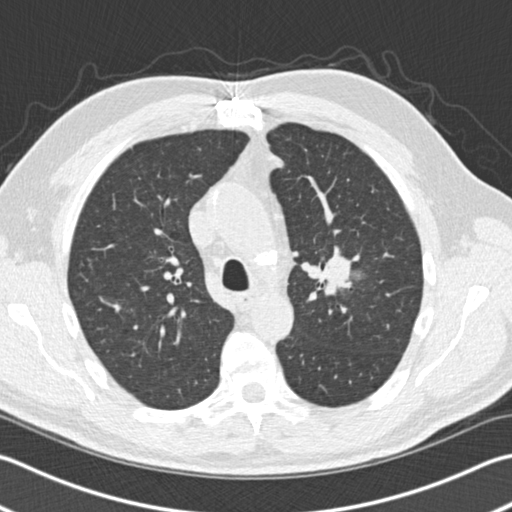
Low-dose screening chest CT, one axial slice. Reconstruction kernel B30f. 120 kVp. Lung window (W 1500 / L -600 HU). 512 × 512 image matrix, field of view 346 × 346 mm.
Structures marked on this image (manually delineated by an expert):
- lesion 1 (tumor, upper lobe of left lung): bounding box (x1, y1, x2, y2) in pixels: (325, 254, 351, 283)